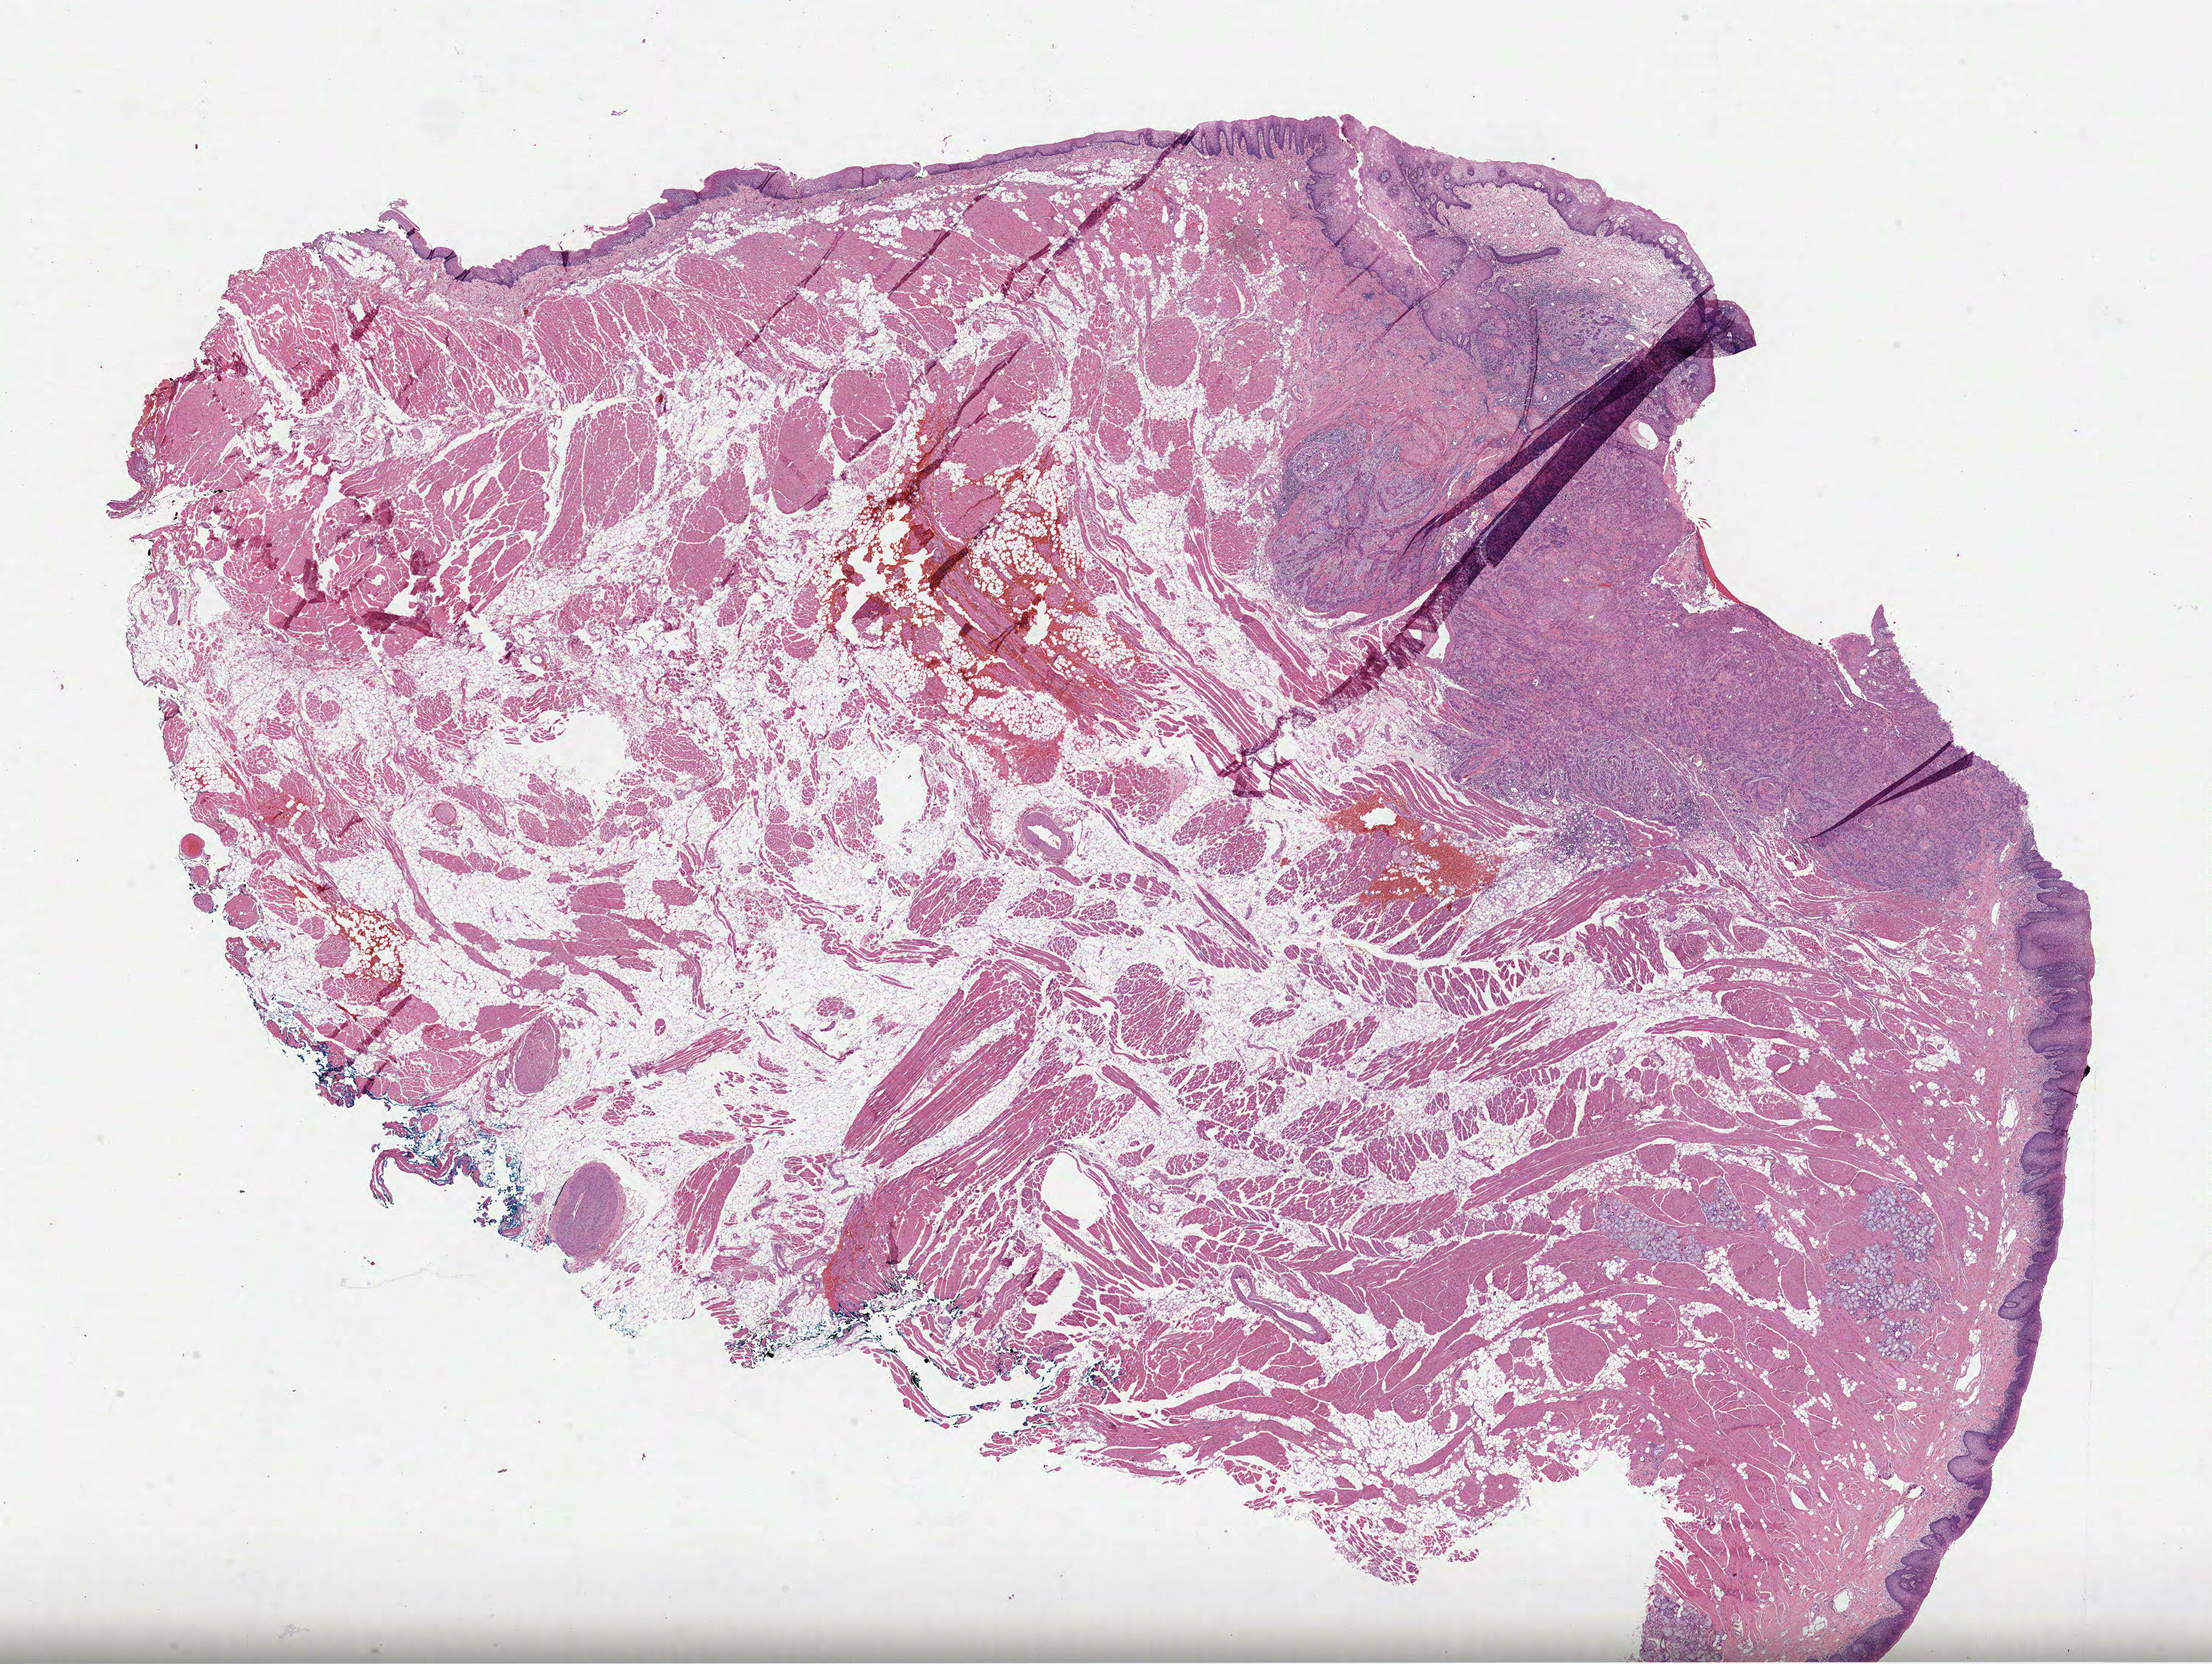
Digitized H&E tissue section (whole slide), shown as a low-resolution overview of the whole scanned area (about 23.9 x 18.0 mm, from a 40x scan). Formalin-fixed paraffin-embedded (FFPE) diagnostic section. Sample: primary tumour, head and neck. Female patient; age at initial diagnosis 61 years. Histologic grade: G2 (moderately differentiated).
Histologic diagnosis: Squamous cell carcinoma, NOS (tongue, NOS). Lymph nodes positive (case pathology): 1 of 1 examined. AJCC pathologic stage: III. Laterality: right.